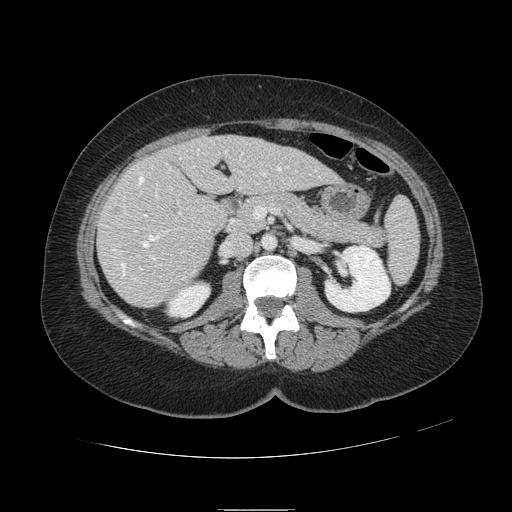
Contrast-enhanced abdominal CT, one axial slice. Slice 44 of 121 in the series (ordered by position). 120 kVp. Soft-tissue window (W 400 / L 40 HU). 2.5 mm slice thickness. 512 × 512 image matrix, field of view 400 × 400 mm. Female patient, age 52 years. Case-level facts recorded for this patient, not image findings: diagnosis: colorectal cancer liver metastases, imaged before liver resection; multiple liver metastases: yes; largest metastasis: 6.3 cm; chemotherapy before resection: yes.
Outlined on this slice (expert manual segmentation):
- hepatic veins: bounding box (x1, y1, x2, y2) in pixels: (113, 149, 281, 278)
- liver: (98, 135, 338, 307)
- planned liver remnant (the part of the liver to remain after resection): (177, 135, 339, 196)
- portal vein (with intrahepatic branches): (140, 201, 182, 269)